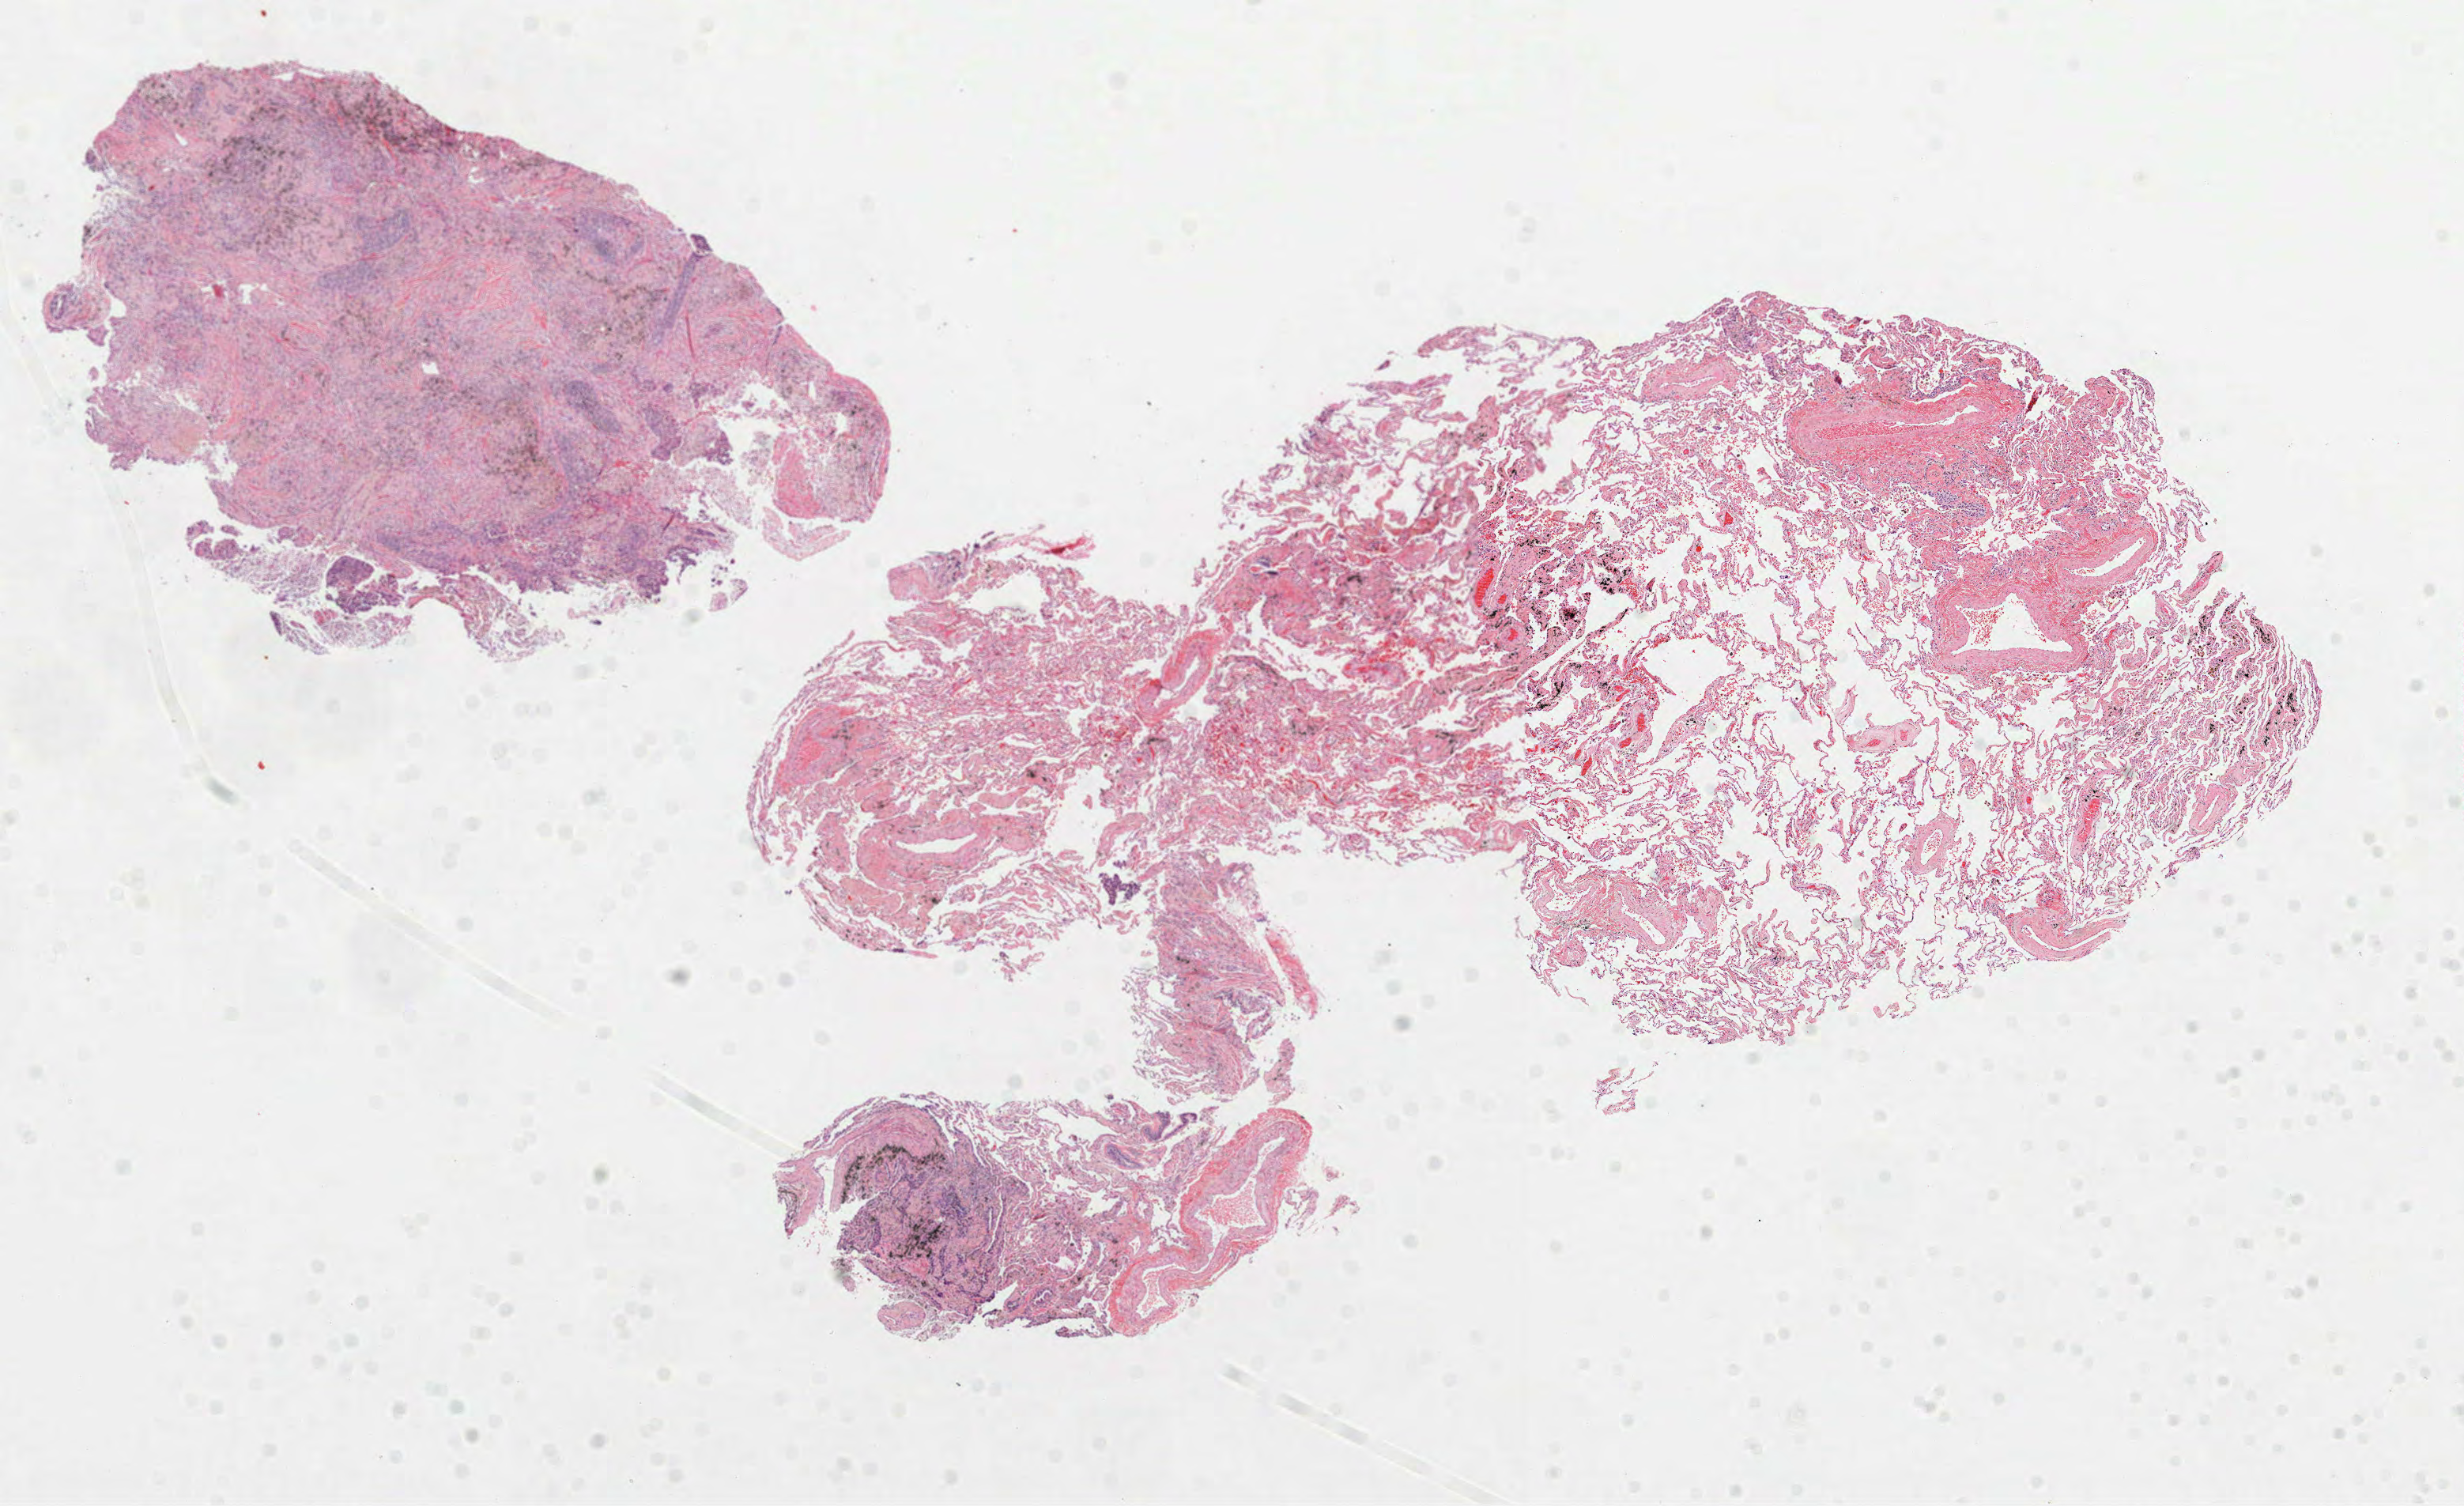
Digitized Hematoxylin and eosin (H&E) stained tissue section (whole slide), shown as a low-resolution overview of the whole scanned area (about 12.6 x 7.7 mm, acquisition: 40x scan), formalin-fixed paraffin-embedded (FFPE) diagnostic section, sample: primary tumour, lung. Male, age 61 years at initial diagnosis.
• AJCC pathologic stage: IA (7th edition)
• histologic diagnosis: Squamous cell carcinoma, NOS (upper lobe, lung)